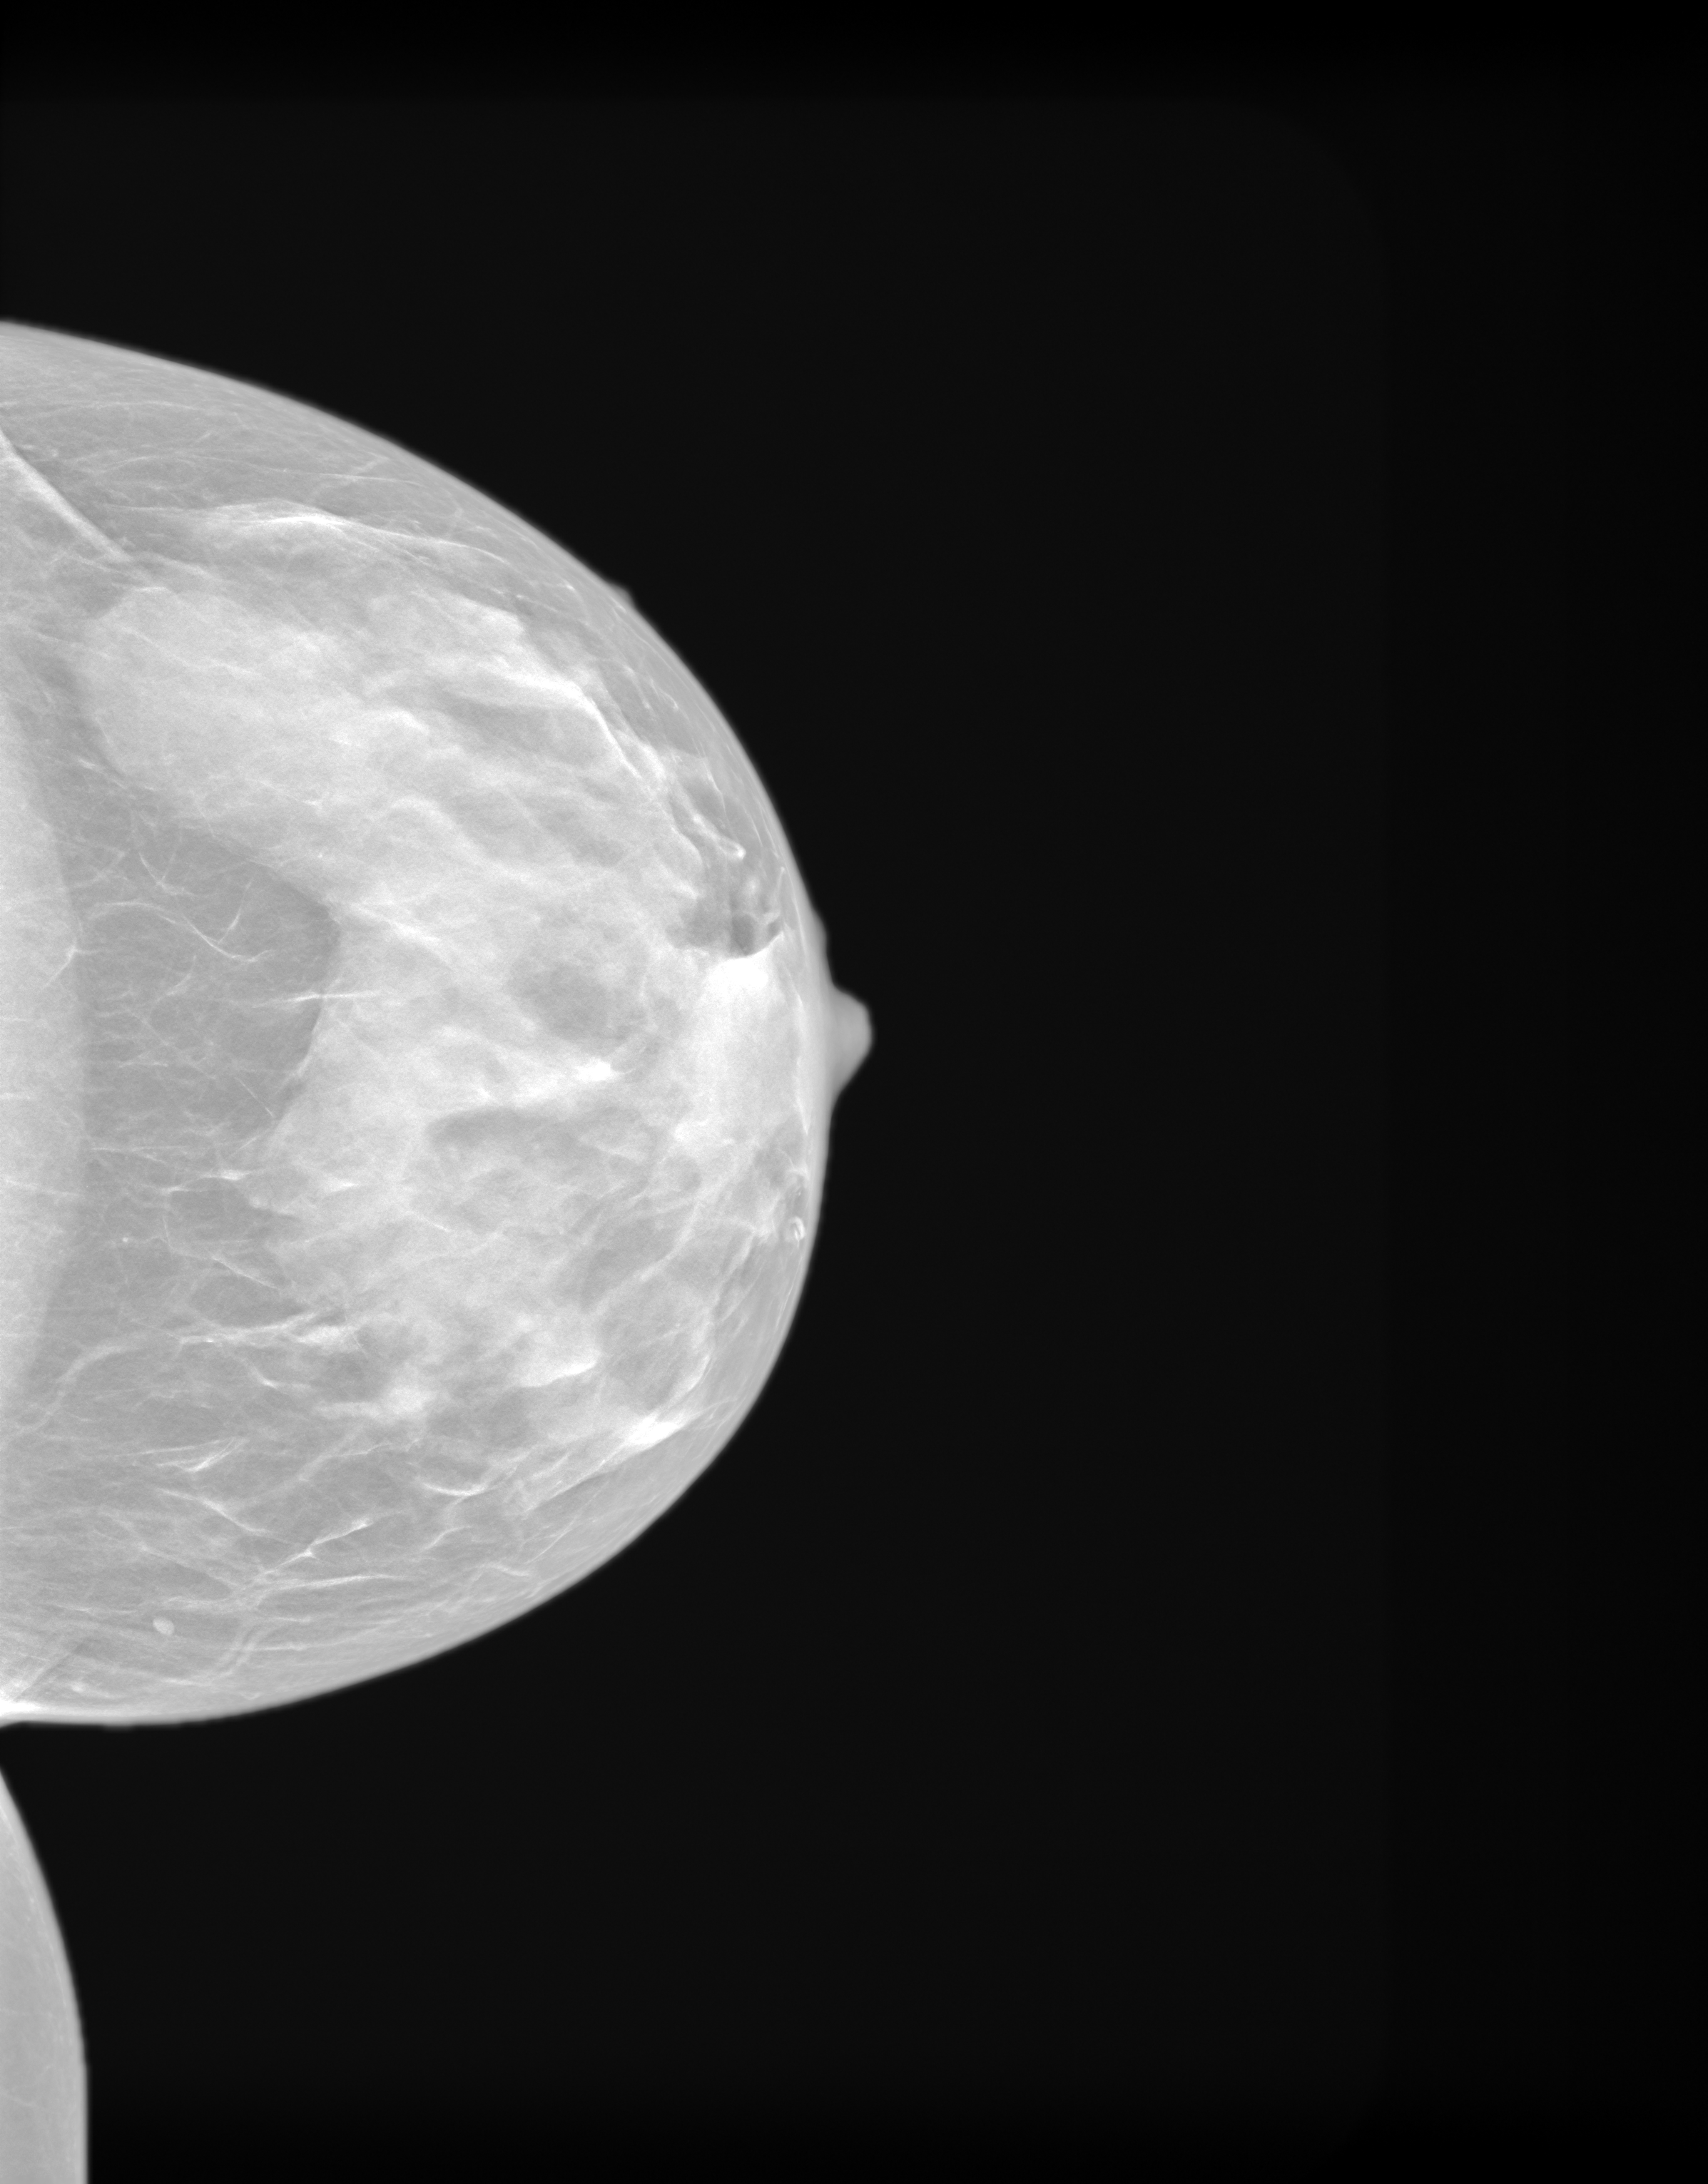
Synthesized 2-D mammogram reconstructed from digital breast tomosynthesis, left breast, CC view, screening examination. Patient aged 60 years (female).
- BI-RADS breast density category at the screening exam (both breasts, scale 1–4): 4
- final BI-RADS category for the screening round (tomosynthesis exam, both breasts): category 1
- recall: no recall after this screen